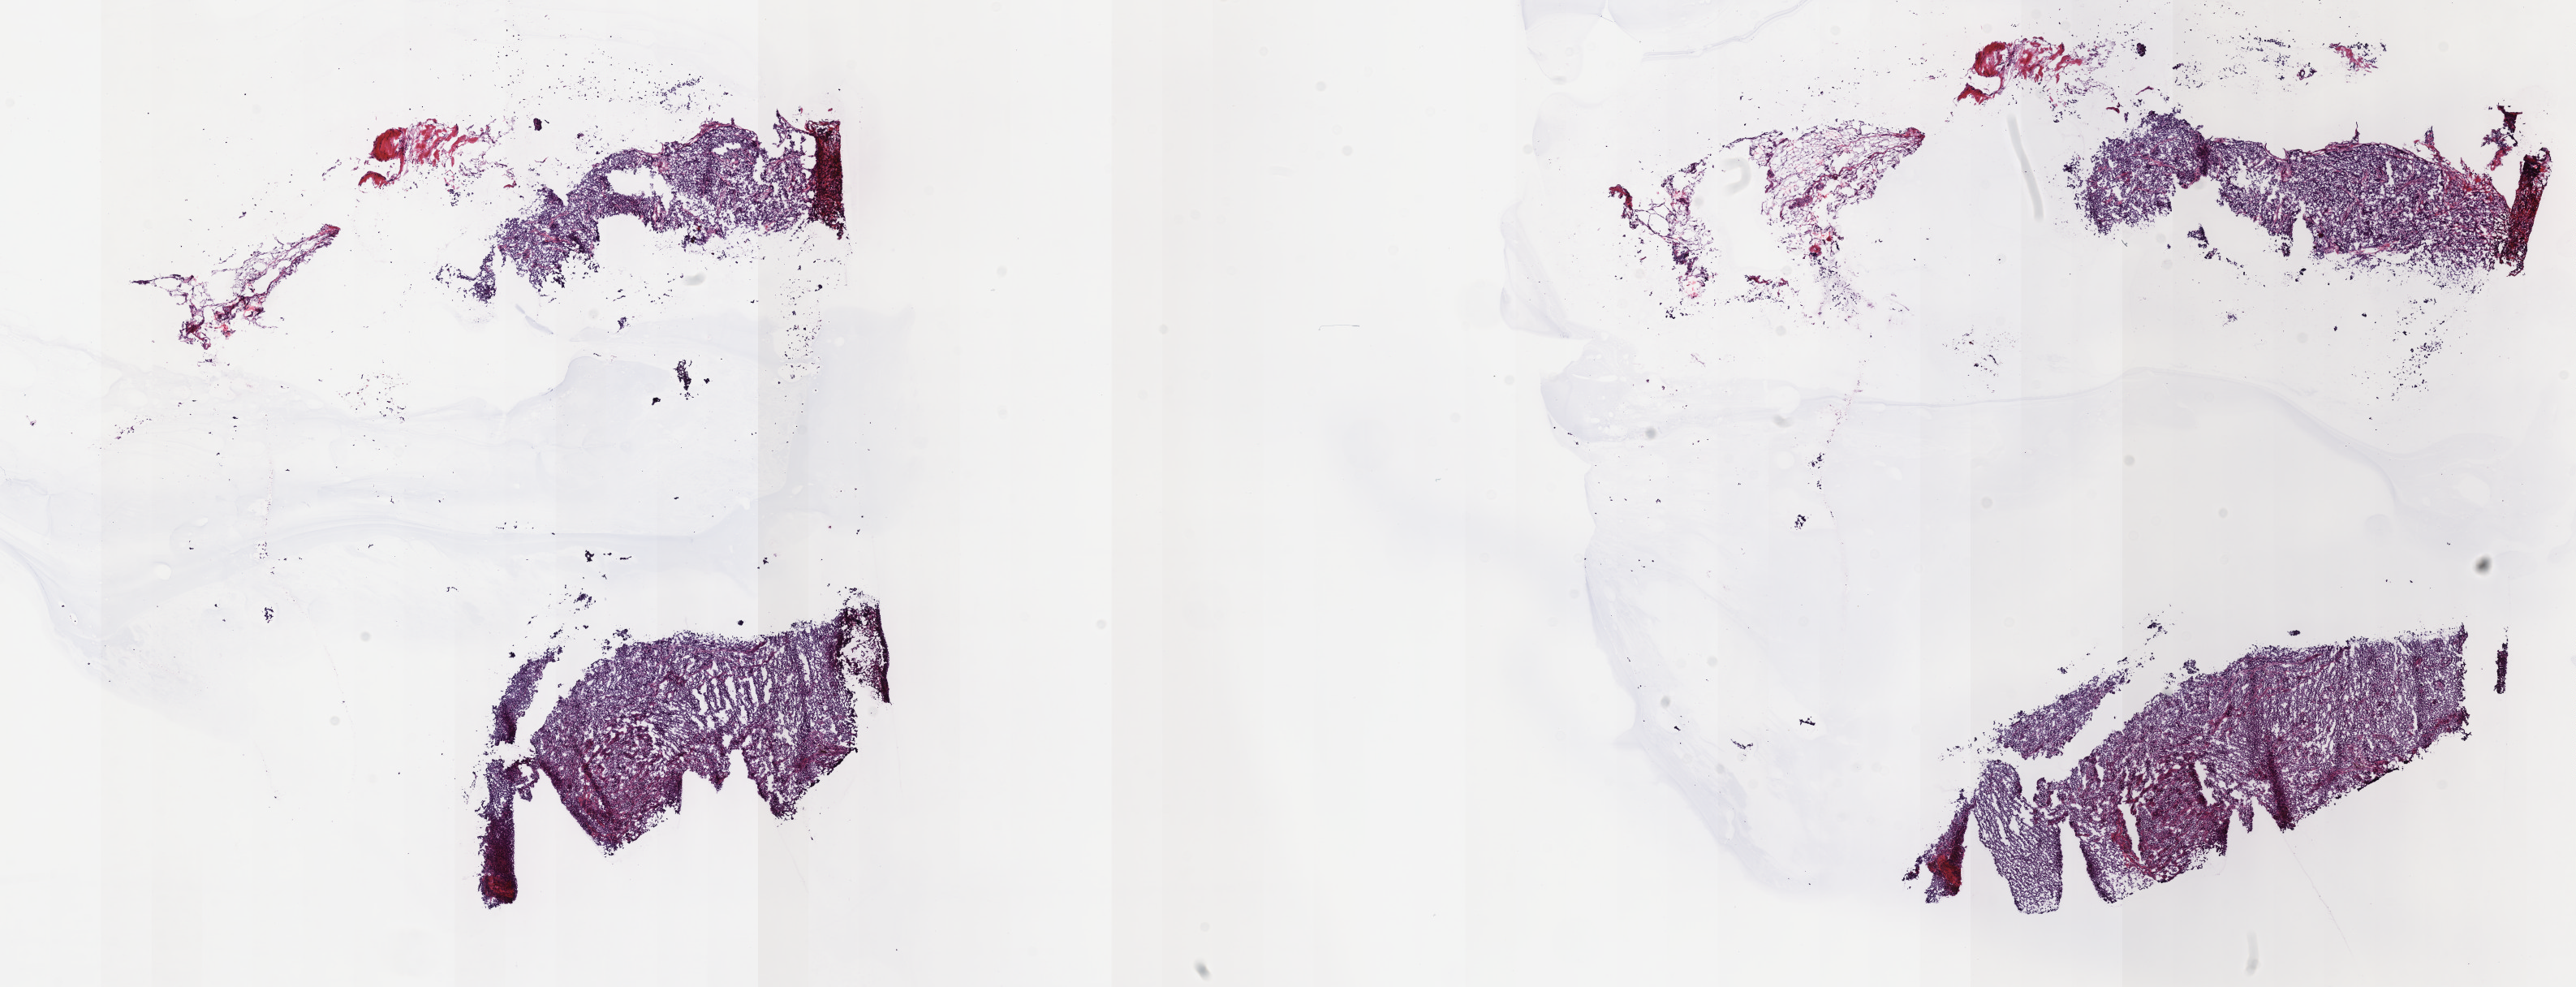
Digitized Hematoxylin and eosin (H&E) stained tissue section (whole slide), shown as a low-resolution overview of the whole scanned area (about 25.7 x 9.8 mm), frozen section from the top of the tissue portion, metastatic tumour sample. Male, age 62 years at initial diagnosis. Pathologist review of this section (percent, as recorded): tumour cells 80%, tumour nuclei 80%, normal cells 0%, stromal cells 20%, necrosis 0%. Inflammatory infiltration, as recorded: lymphocyte infiltration 4%, monocyte infiltration 1%, neutrophil infiltration 1%.
• this section: metastatic tumour tissue
• patient diagnosis: Malignant melanoma, NOS